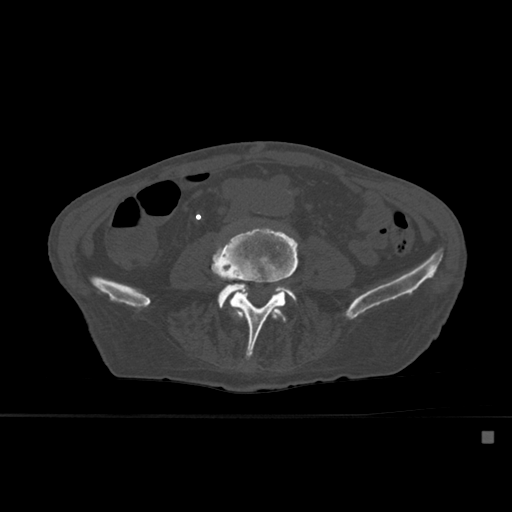
CT including the spine, one axial slice. Slice 192 of 527 in the series (ordered by position). Bone window (W 1800 / L 400 HU). 1.5 mm slice thickness. 512 × 512 image matrix, field of view 373 × 373 mm. Male patient, age 78 years. Case-level facts recorded for this patient, not image findings: primary cancer: prostate.
Annotated regions visible in this slice (semi-automatic segmentation, software-assisted and operator-edited):
- L3 vertebra: bounding box [x1, y1, x2, y2] px = [231, 309, 287, 323]
- L4 vertebra: [212, 227, 298, 358]
- L5 vertebra: [217, 283, 297, 308]